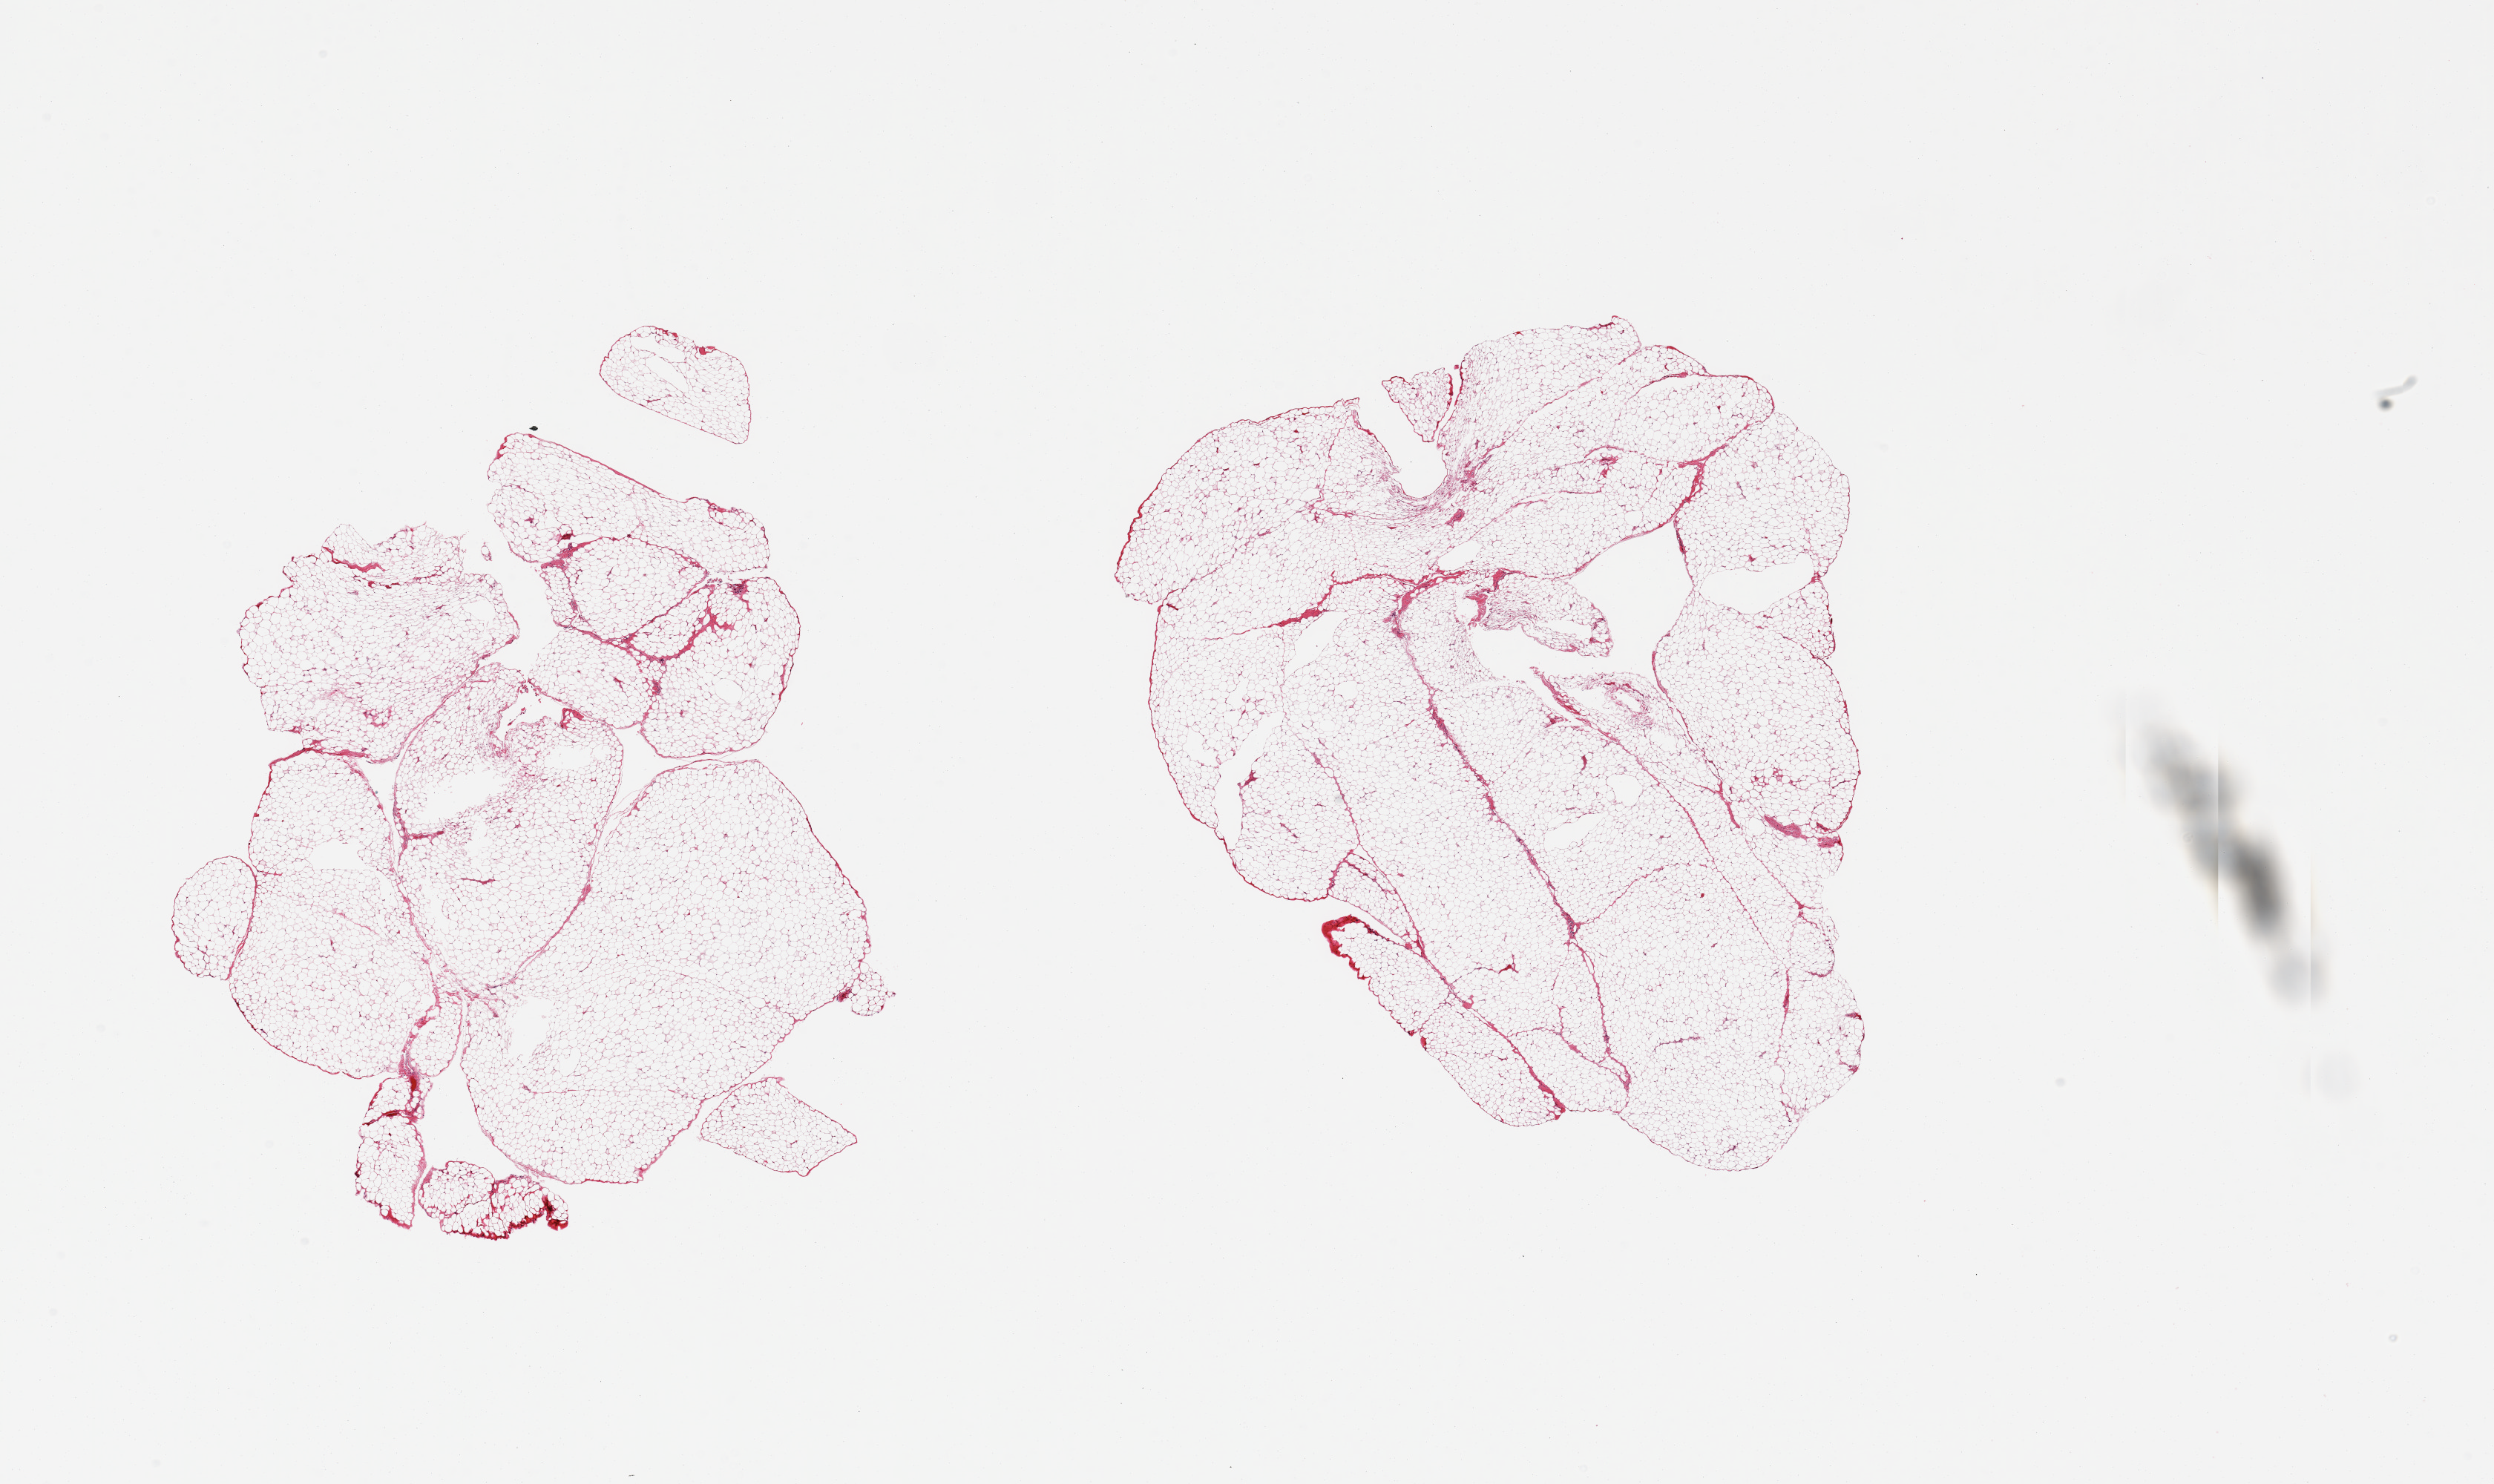
Whole-slide image, H&E stain, brightfield — shown as a low-resolution overview of the whole scanned area (about 26.6 x 15.8 mm); PAXgene-fixed, paraffin-embedded tissue; sampled site (target tissue): omentum; tissue donor sample. Donor: male.
Review note (as recorded): 2 pieces; lobulated fat with virtually no fibrous content.